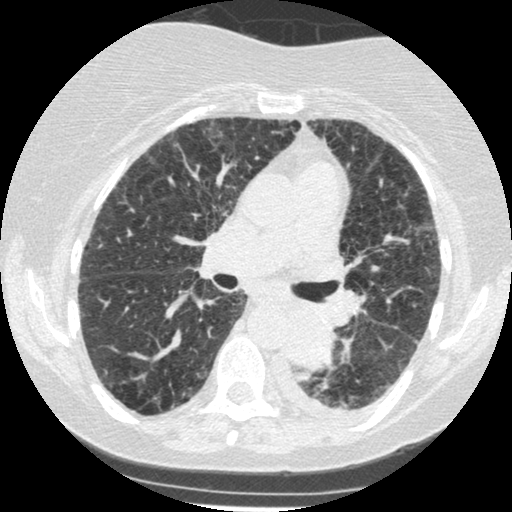
Low-dose screening chest CT, axial slice; third annual screen; lung window (W 1500 / L -600 HU); slice 196 of 341 in the series. Female, age 60 years at enrolment. Former smoker at enrolment.
Lesion marked by an expert reader, bounding box <270,307,341,373> (left, top, right, bottom; pixels). Screening reader's record for this exam (one nodule recorded; not confirmed to be the boxed lesion): non-calcified nodule or mass ≥4 mm, left lower lobe, 54 × 38 mm, smooth margins, soft tissue attenuation, pre-existing on the prior screen: yes; interval growth: yes. Official screen result: positive, other. Later outcome: lung cancer diagnosed 15 days after this screen — small cell carcinoma, NOS, left lower lobe, undifferentiated (G4), stage IV (AJCC 6th edition), 69 mm at pathology.